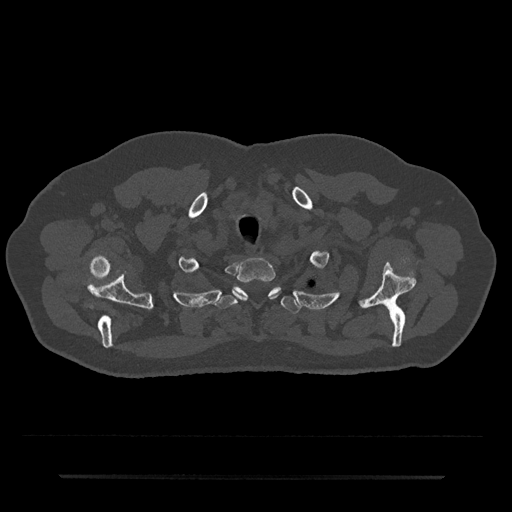
CT including the spine, one axial slice; slice 624 of 797 in the series (ordered by position); bone window (W 1800 / L 400 HU); 0.5 mm slice thickness; 512 × 512 image matrix, field of view 437 × 437 mm. Male patient, age 69 years. From the clinical record (not read from this slice): primary cancer: prostate.
Outlined on this slice (semi-automatic segmentation, software-assisted and operator-edited):
- T1 vertebra: bounding box [x1, y1, x2, y2] px = [233, 258, 281, 299]
- T2 vertebra: [216, 287, 300, 313]